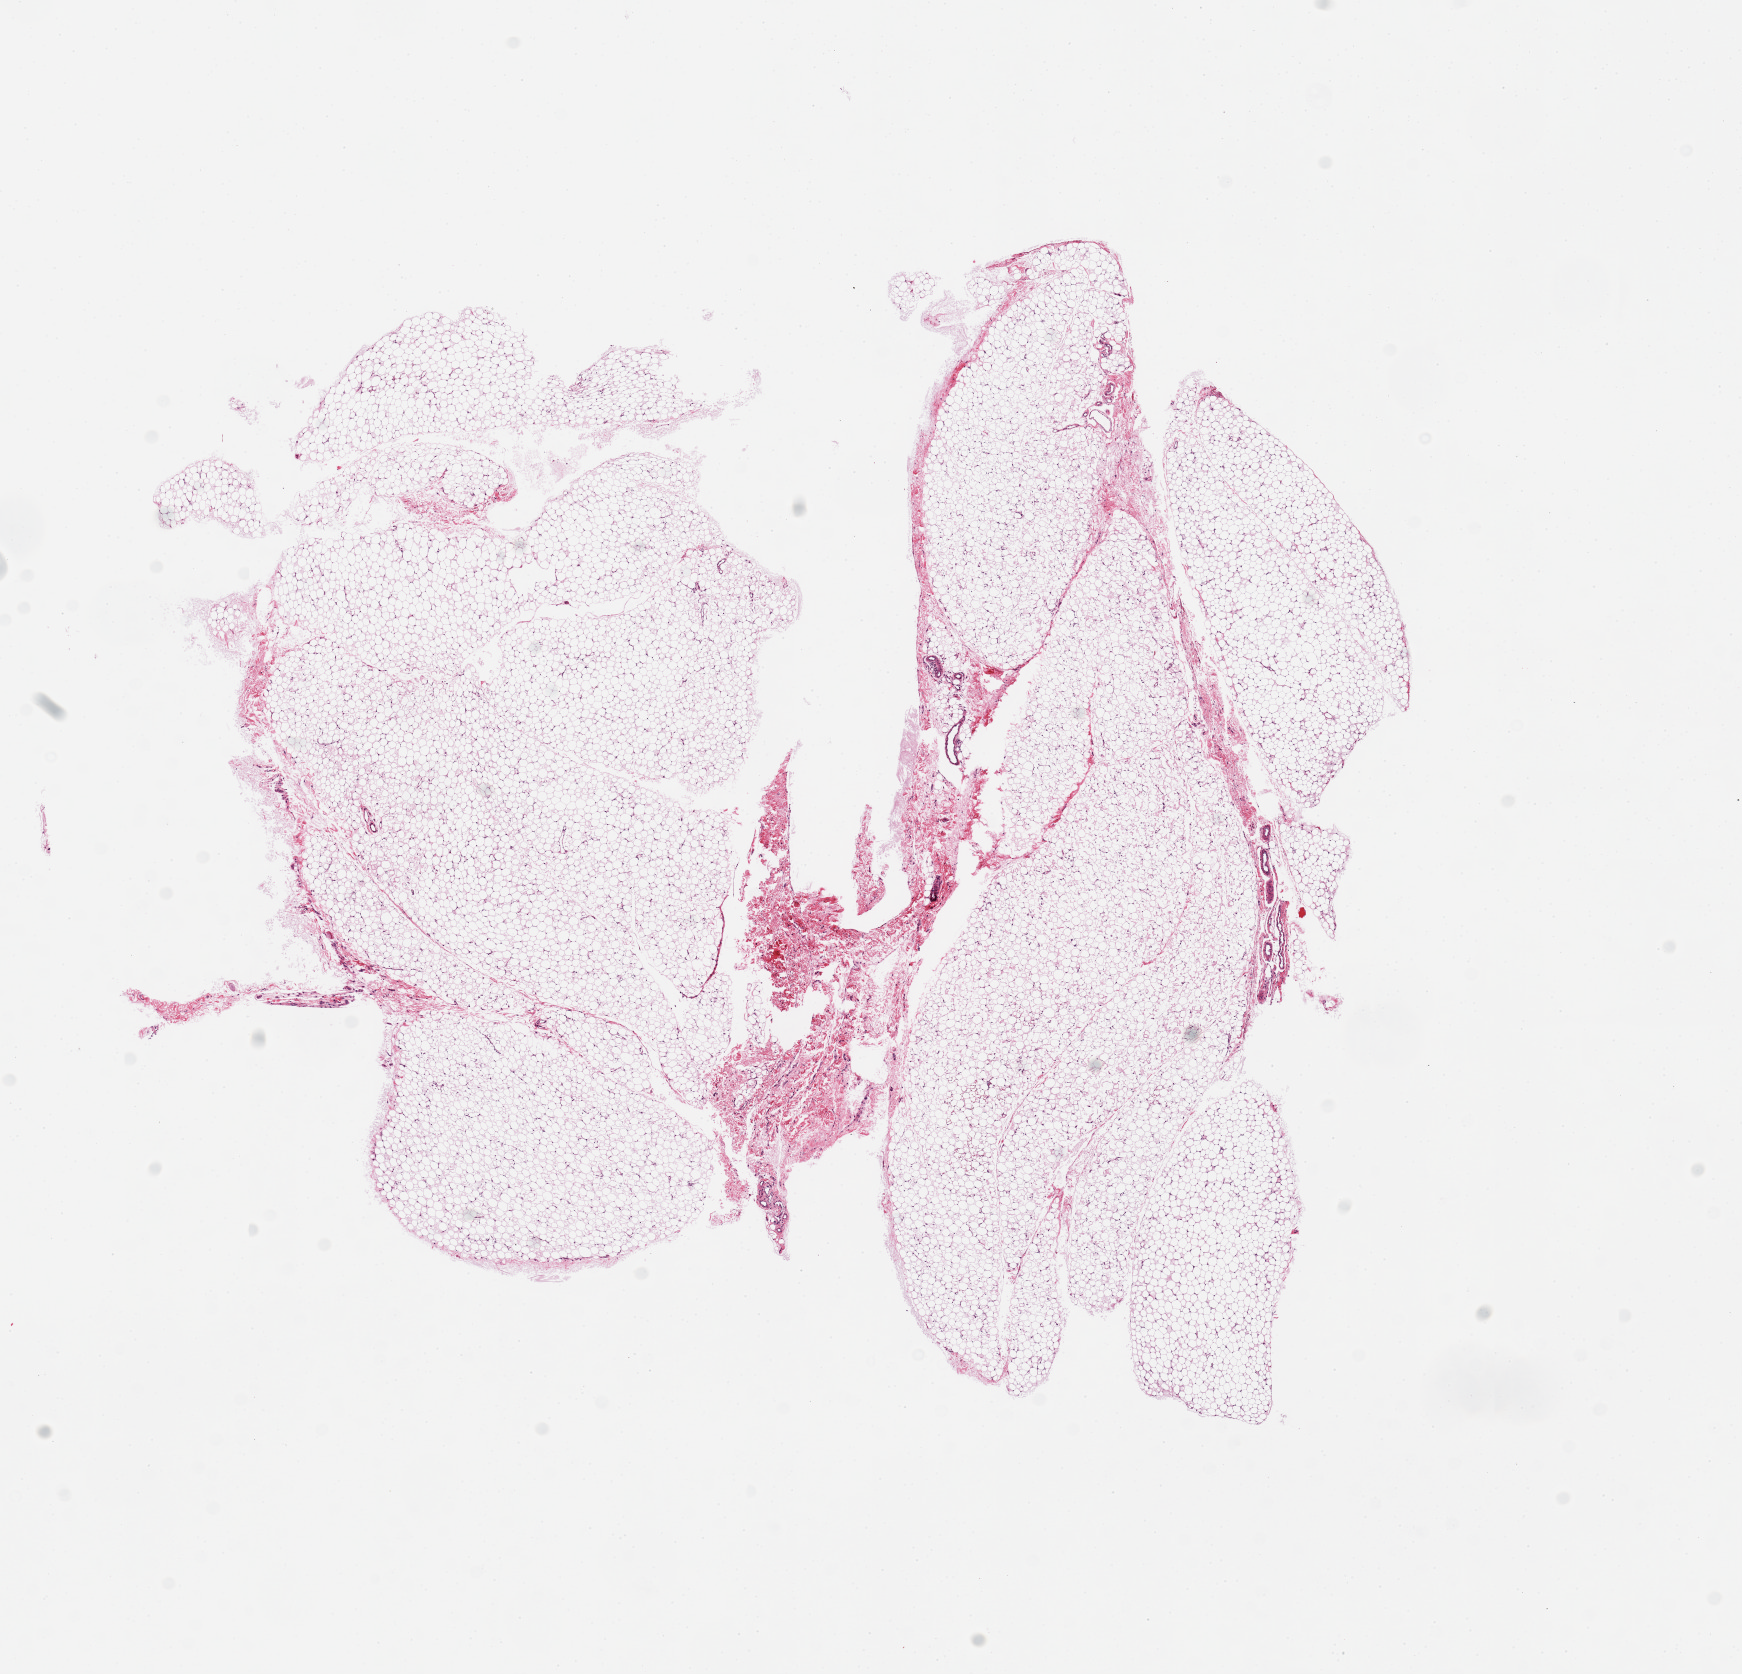
H&E whole-slide image — whole scanned area (about 13.8 x 13.2 mm) shown as a low-resolution overview, PAXgene-fixed, paraffin-embedded tissue, target tissue: adrenal gland, tissue donor sample. Donor: female.
Reviewer comment on this tissue sample: 2 pieces, adipose tissue, no adrenal.